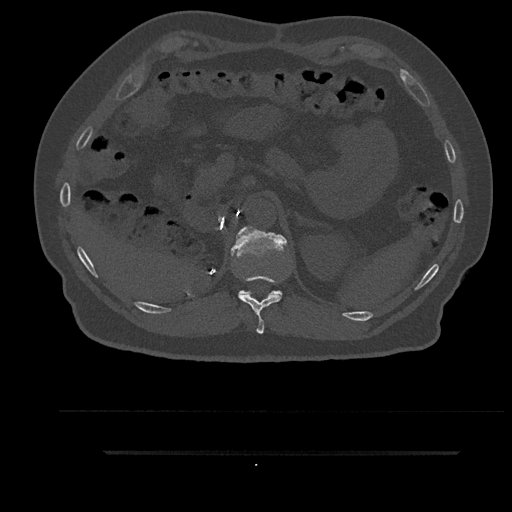
CT including the spine, one axial slice. Slice 278 of 797 in the series (ordered by position). Reconstruction kernel Br40s/3. 120 kVp. Bone window (W 1800 / L 400 HU). 0.5 mm slice thickness. 512 × 512 image matrix, field of view 432 × 432 mm. Male patient, age 63 years. From the clinical record (not read from this slice): primary cancer: renal.
Annotated regions visible in this slice (semi-automatic segmentation, software-assisted and operator-edited):
- T11 vertebra: bounding box (x1, y1, x2, y2) in pixels: (238, 253, 282, 334)
- T12 vertebra: (231, 226, 287, 296)